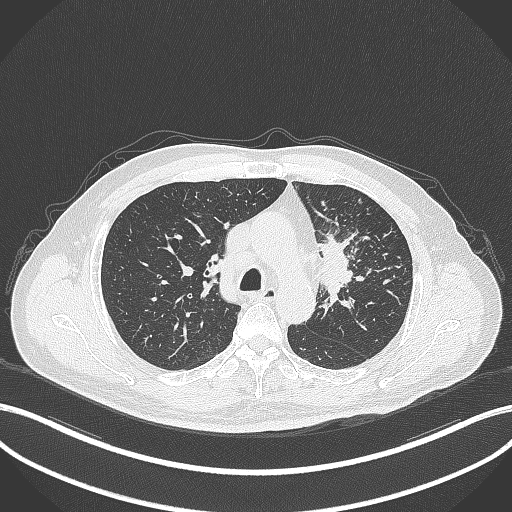
Chest CT, one axial slice. Position 242 of 386 along the scan axis. Lung window (W 1500 / L -600 HU). 1 mm slice thickness. 512 × 512 image matrix. Male patient, age 69 years. From the clinical record (not read from this slice): clinical TNM (as recorded): T2a N2 M0; histopathological grade: G2-3.
Annotated regions visible in this slice (rectangle marked by the reading radiologist):
- lung tumour (recorded histology: adenocarcinoma): box from (x=319, y=235) to (x=357, y=308) px